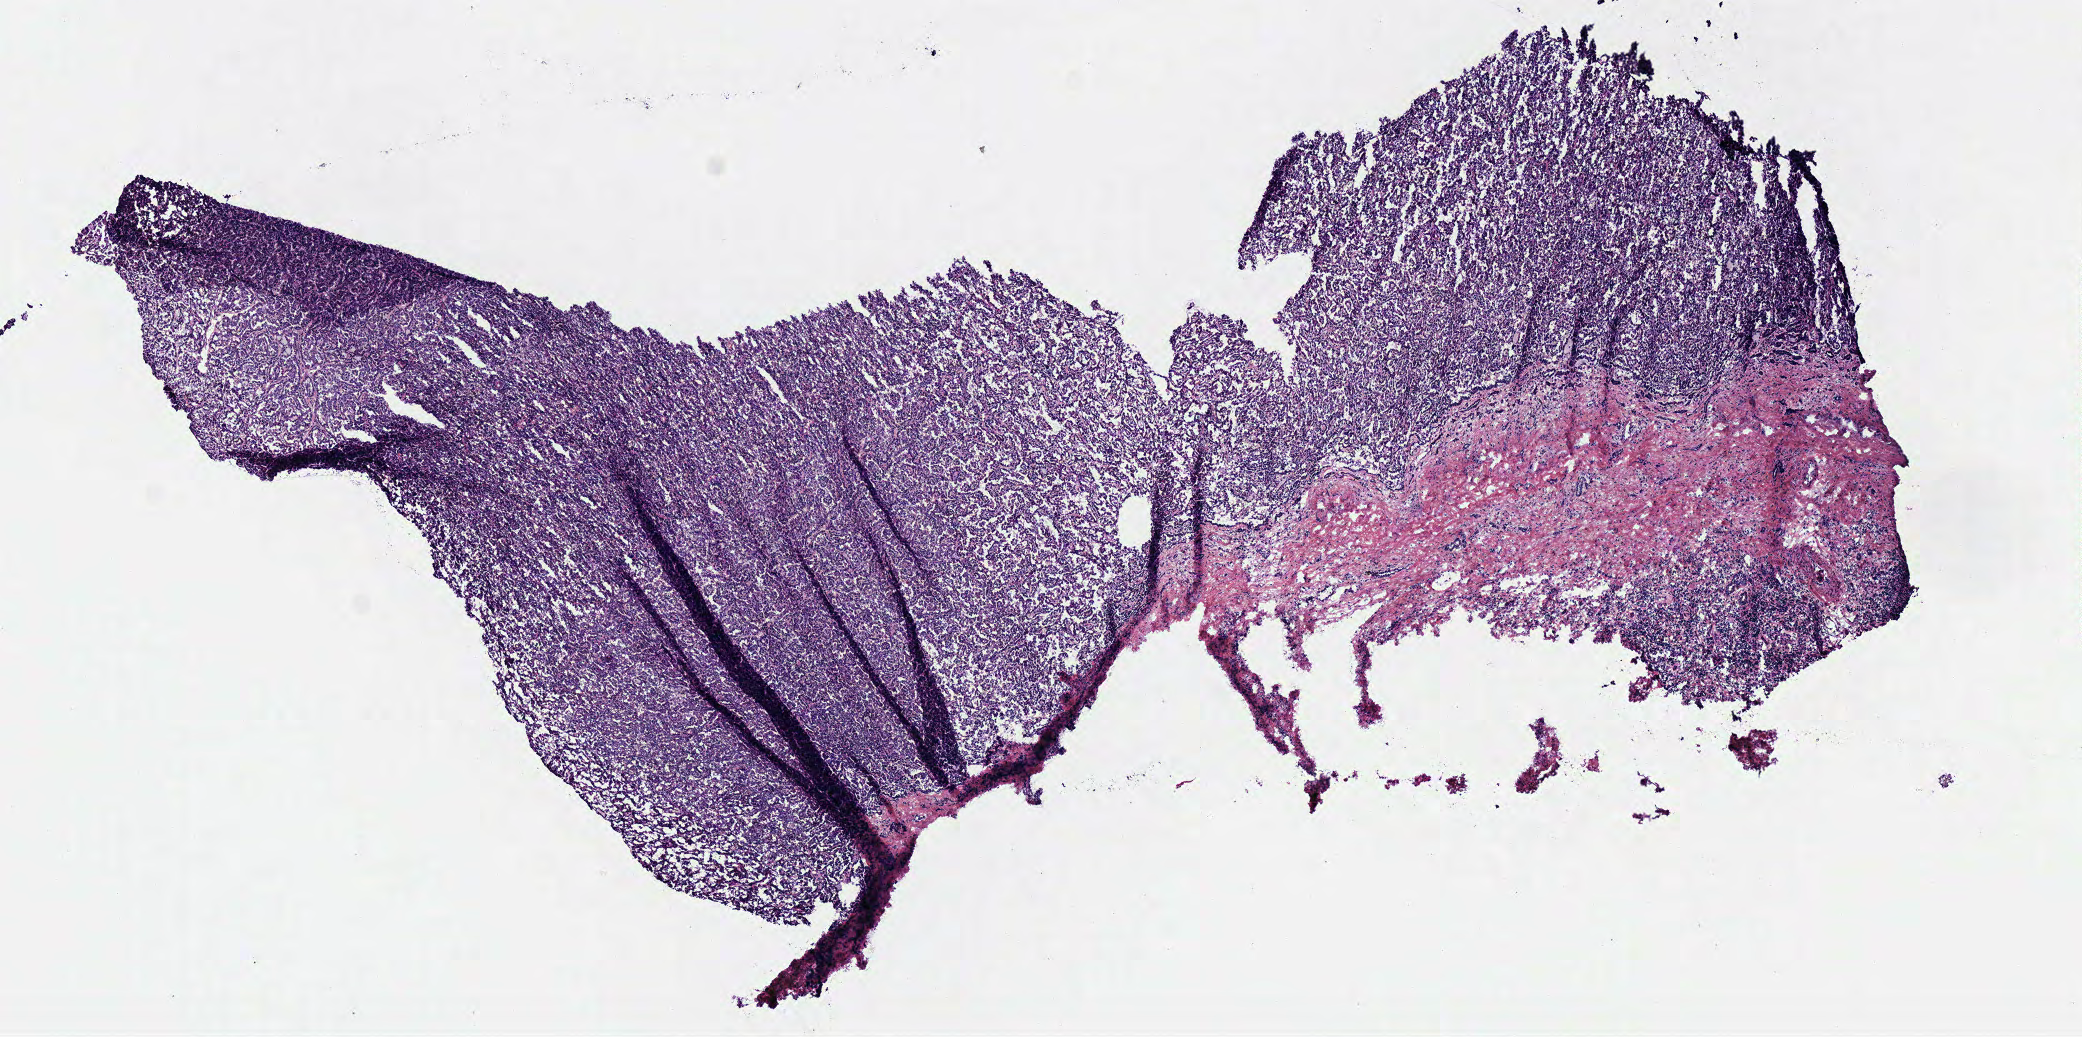
H&E whole-slide image — whole scanned area (about 8.2 x 4.1 mm, from a 40x scan) shown as a low-resolution overview, frozen section from the bottom of the tissue portion, kidney, primary tumour sample. Patient: male, age at initial diagnosis 45 years. Slide review estimates, as recorded: tumour cells 80%, tumour nuclei 85%, normal cells 0%, stromal cells 20%, necrosis 0%.
AJCC pathologic stage: I (6th edition). Diagnosis: Papillary adenocarcinoma, NOS.